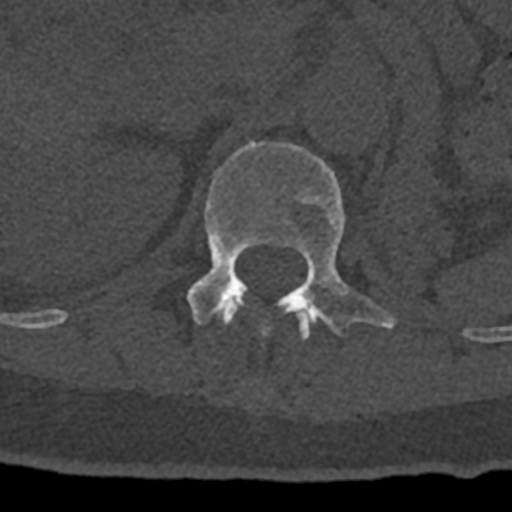
CT including the spine, one axial slice. Slice 448 of 797 in the series (ordered by position). Bone window (W 1800 / L 400 HU). 512 × 512 image matrix, field of view 160 × 160 mm. Patient: male, 74 years. Case-level facts recorded for this patient, not image findings: primary cancer: renal; vertebrae with lytic lesions (as recorded): T10, L1, L2, L3, L4, L5.
Outlined on this slice (semi-automatic segmentation, software-assisted and operator-edited):
- L1 vertebra: box from (x=186, y=141) to (x=396, y=347) px
- T12 vertebra: (x=220, y=297)–(x=315, y=339)